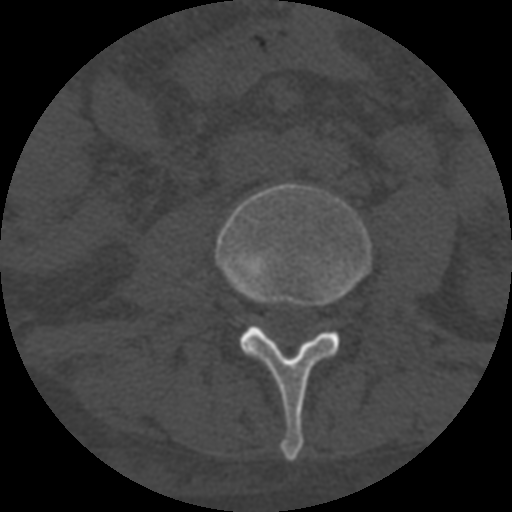
CT including the spine, one axial slice. Slice 227 of 708 in the series (ordered by position). Reconstruction kernel STANDARD. 120 kVp. One of 3 acquisitions stored at this slice position. Bone window (W 1800 / L 400 HU). 1.25 mm slice thickness. 512 × 512 image matrix. Patient age 55 years. Case-level facts recorded for this patient, not image findings: primary cancer: colon; vertebrae with lytic lesions (as recorded): T12, L1, L5.
Outlined on this slice (semi-automatically segmented with operator editing):
- L3 vertebra: box from (x=216, y=183) to (x=372, y=461) px